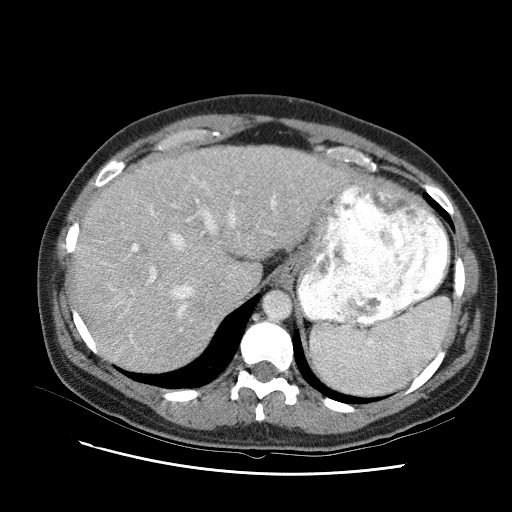
Contrast-enhanced abdominal CT (liver protocol), one axial slice; position 71 of 95 along the scan axis; reconstruction kernel STANDARD; 120 kVp; one of 2 acquisitions stored at this slice position; soft-tissue window (W 400 / L 40 HU); 512 × 512 image matrix. Case-level facts recorded for this patient, not image findings: diagnosis: hepatocellular carcinoma (patient treated with transarterial chemoembolisation; whether this scan precedes or follows treatment is not stated here); TNM stage (as recorded): Stage-I; Child-Pugh class: B; tumour differentiation: moderately differentiated; tumour nodularity: uninodular.
Structures marked on this image (semi-automatic segmentation, software-assisted and operator-edited):
- liver parenchyma outside the tumour (the mass and vessels are separate outlines, so this box may not span the whole liver): bounding box [x1, y1, x2, y2] px = [68, 142, 350, 356]
- liver vessels: [95, 178, 312, 315]